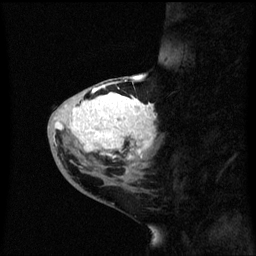
Breast MRI (dynamic contrast-enhanced), one sagittal slice; position 22 of 60 along the scan axis; dynamic contrast-enhanced series, image 2 of 3 at this slice position (ordered by acquisition); 1.5 T; TE 4.2 ms, TR 8.4 ms; 2.3 mm slice thickness; 256 × 256 image matrix, field of view 200 × 200 mm. Patient: female, 46 years. From the clinical record (not read from this slice): setting: breast cancer imaged before/during neoadjuvant chemotherapy; receptor status: HER2-positive.
Annotated regions visible in this slice (semi-automatically segmented with operator editing):
- analysis volume of interest (the breast-tissue region the enhancement analysis was run in; not a lesion): bounding box <48,86,161,171> (left, top, right, bottom; pixels)
- tumour enhancement mask (voxels above the 70 % enhancement threshold inside the analysis volume of interest): <56,88,155,161>